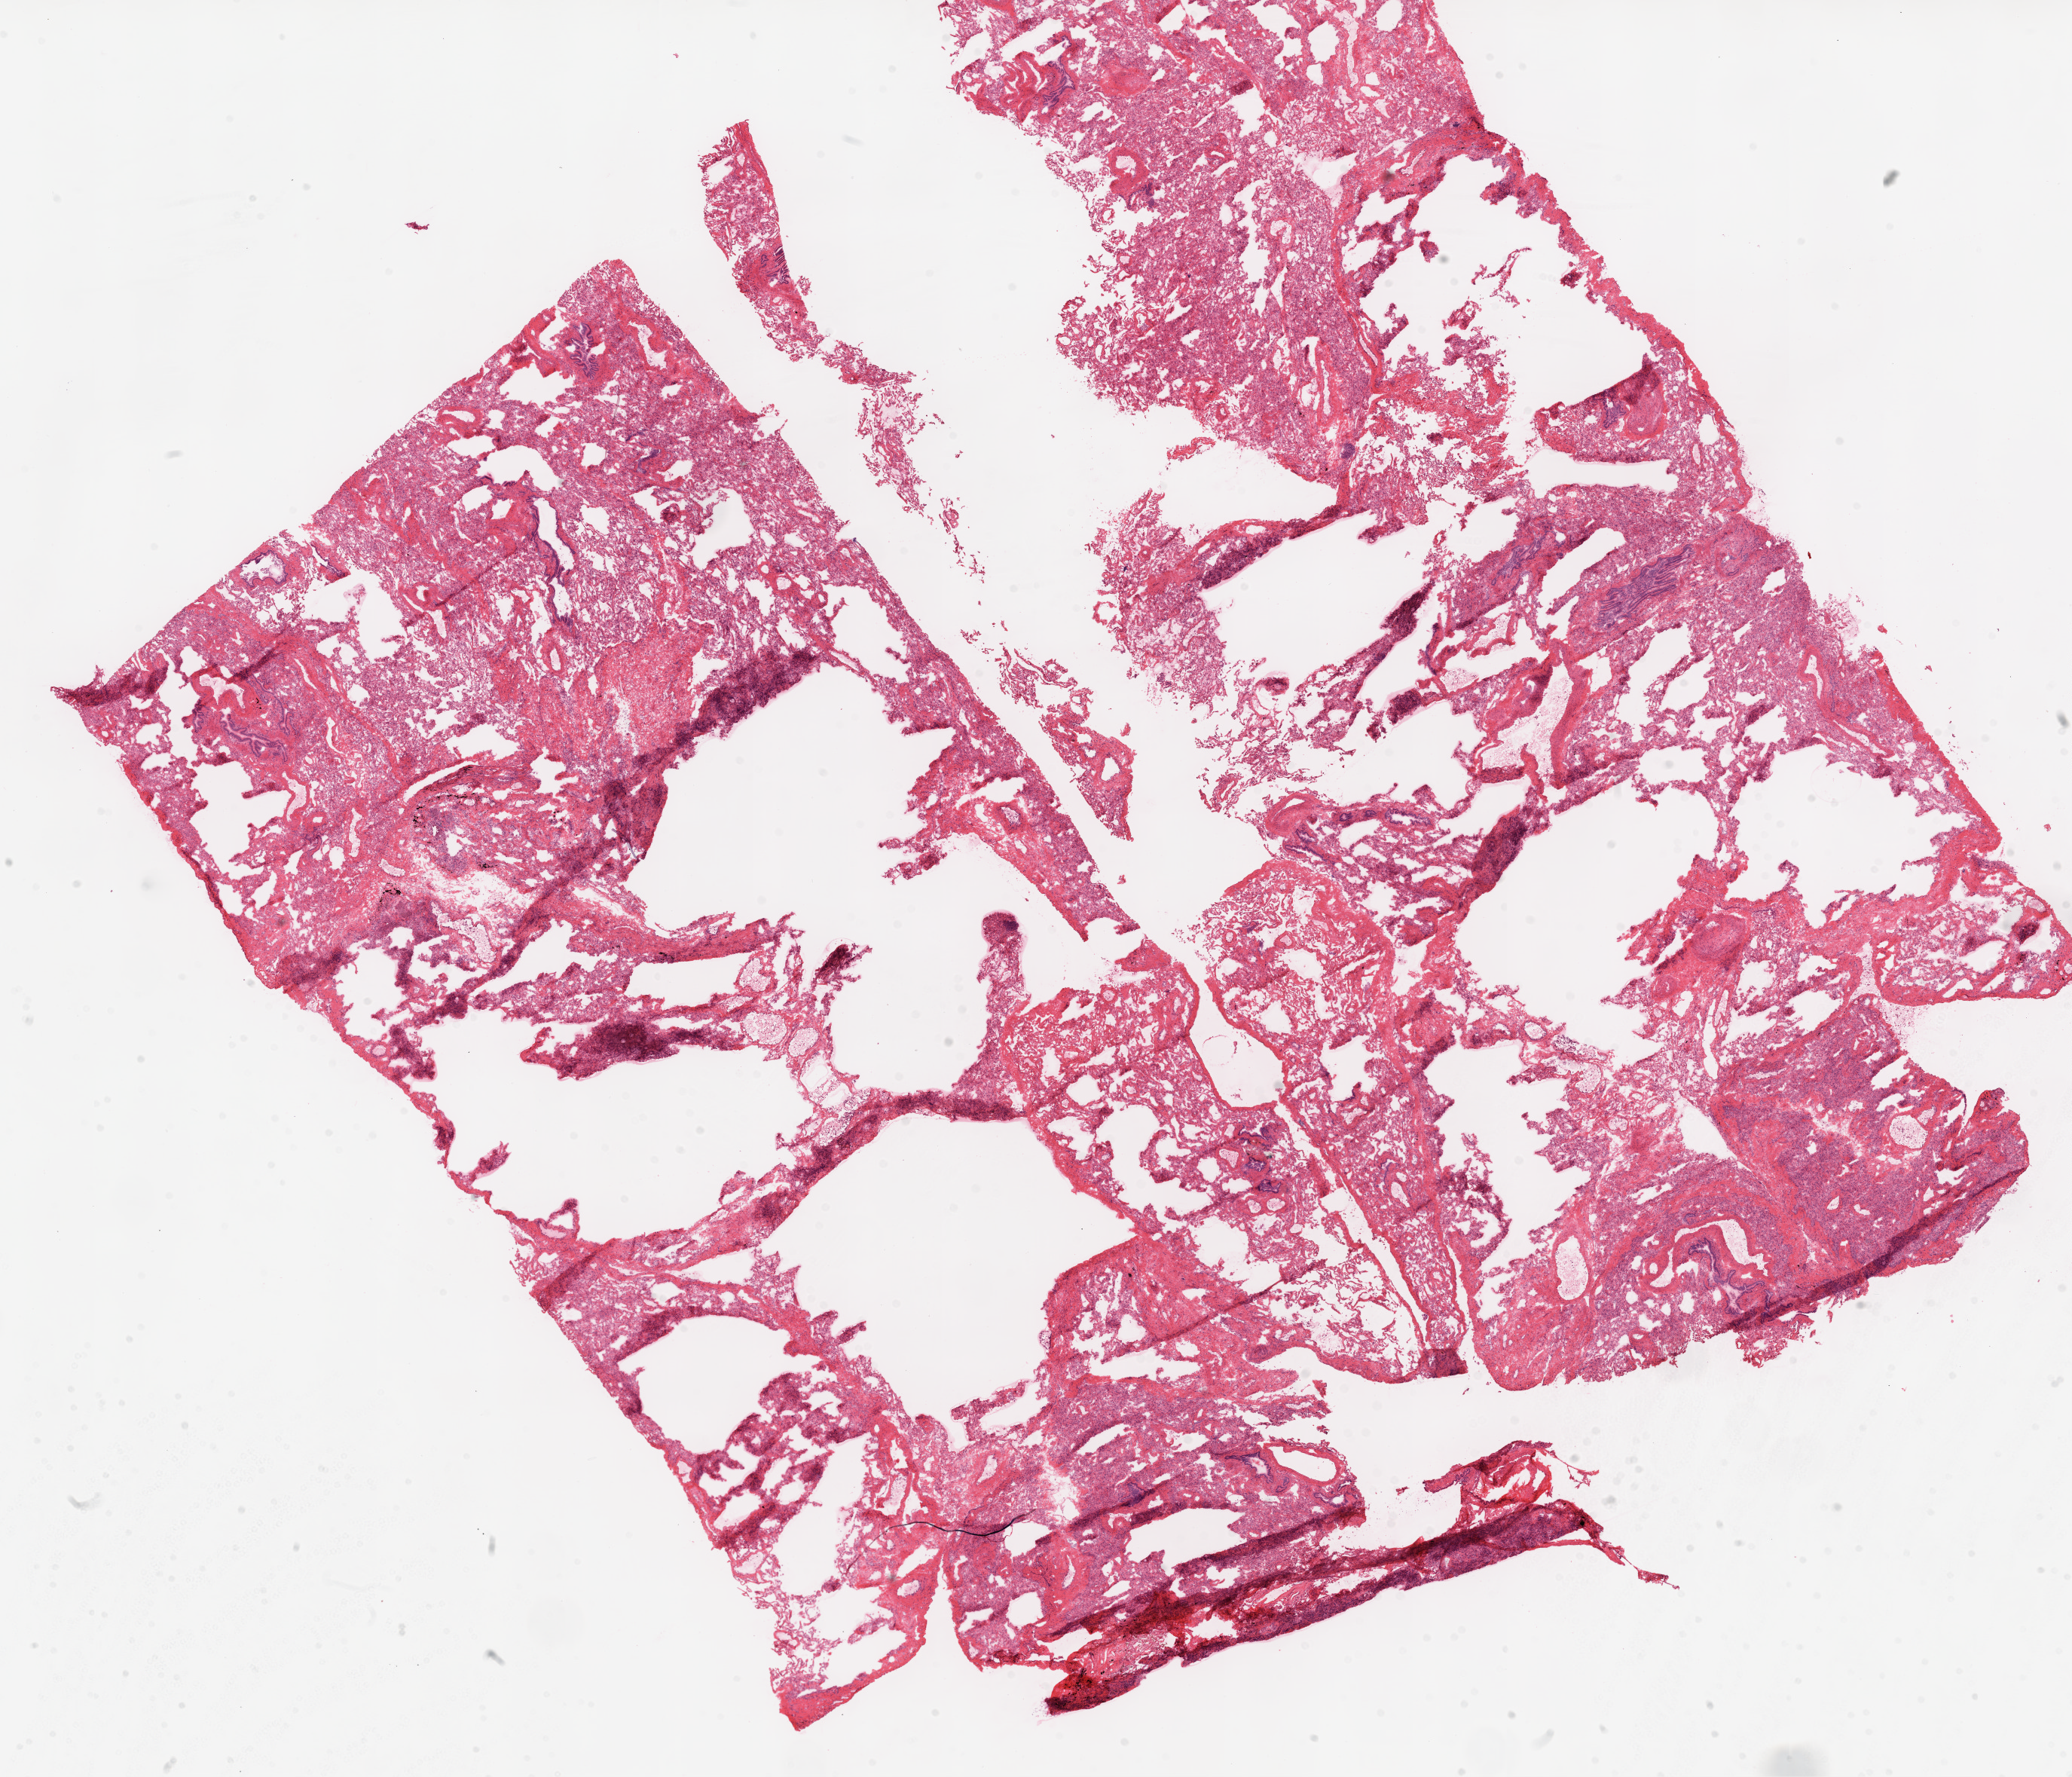
Digitized H&E-stained tissue section (whole slide), low-resolution overview of the scanned area, about 22.1 x 18.9 mm, frozen section, sample: solid tissue normal (non-tumour tissue), lung. Male, age 70 years at initial diagnosis.
This section: solid tissue normal (non-tumour) sample from the same patient. Patient diagnosis: Squamous cell carcinoma, NOS (upper lobe, lung).